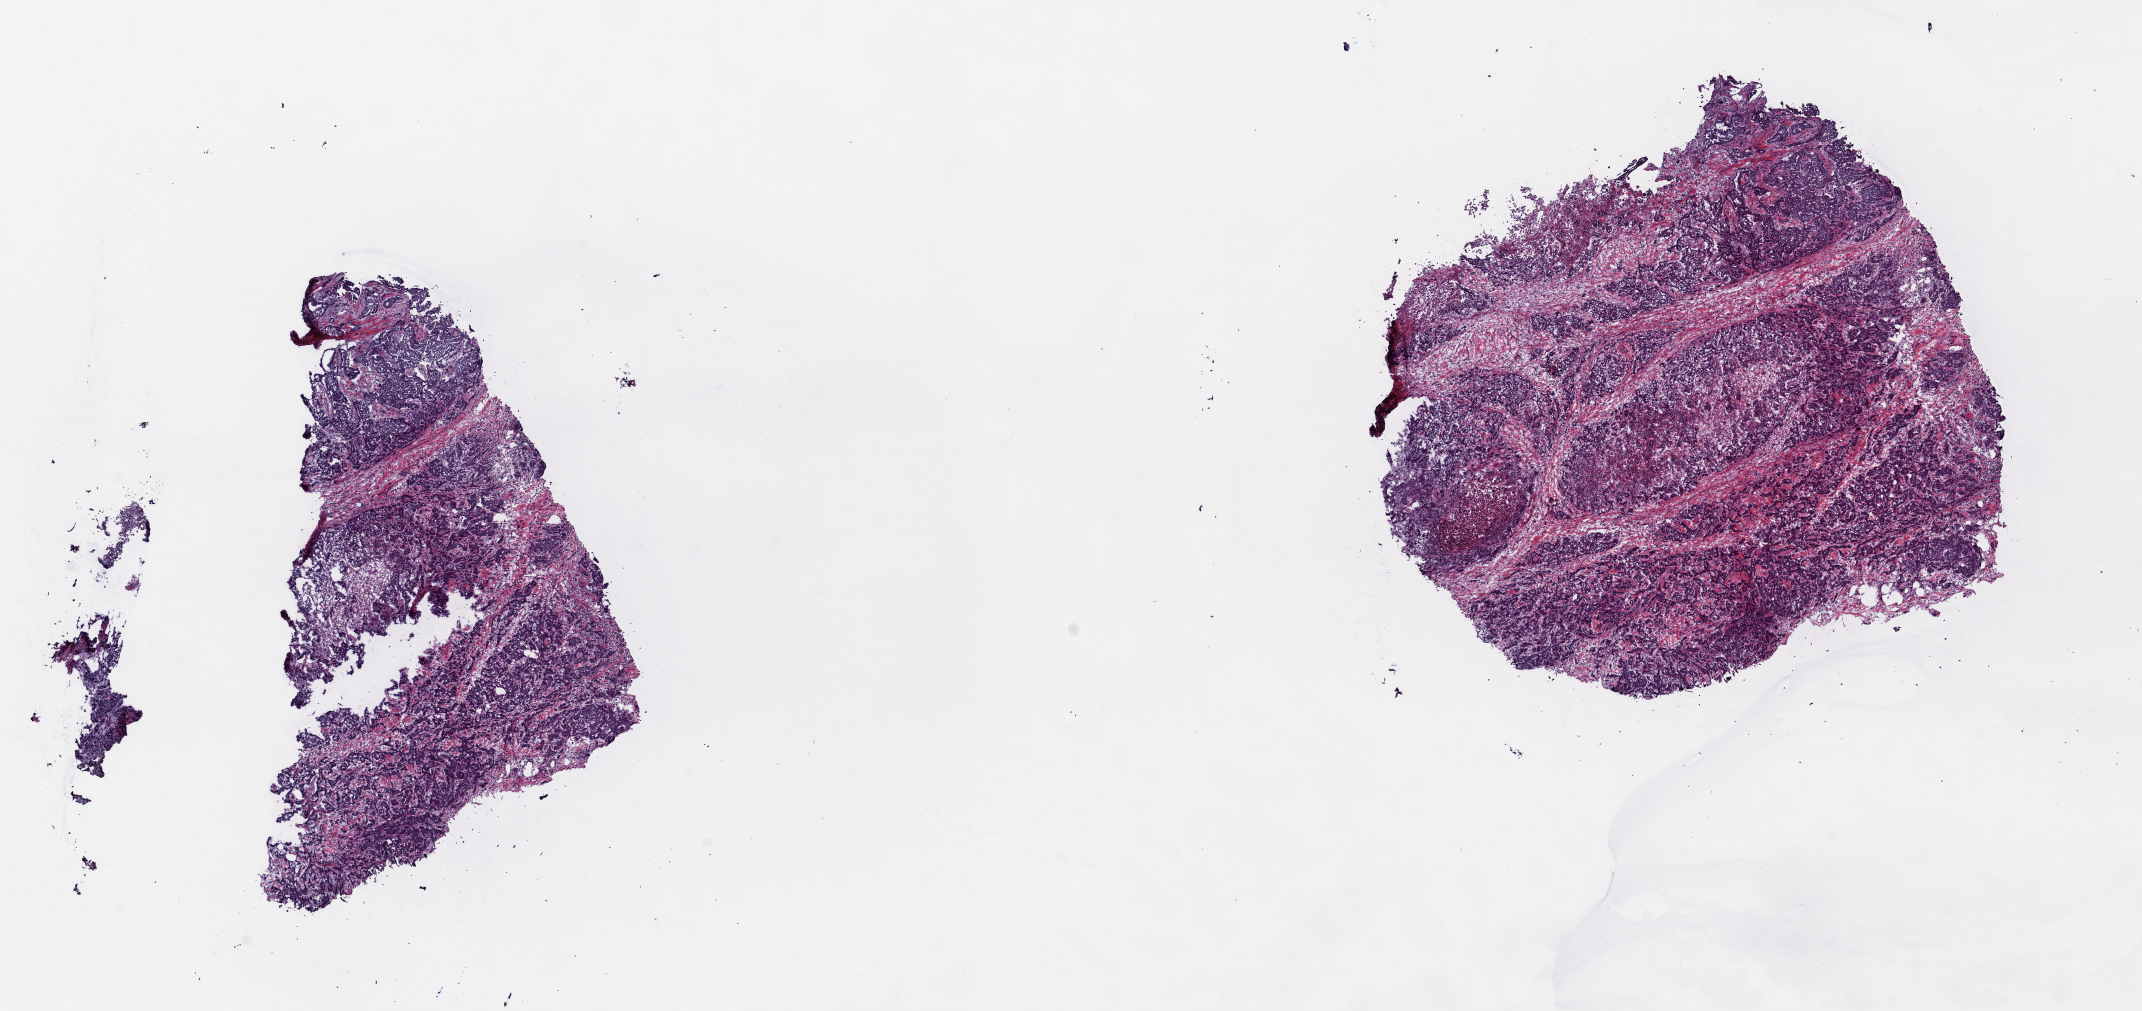
Whole-slide histology image, Hematoxylin and eosin (H&E) stained — a low-resolution overview of the entire scanned area, about 16.8 x 7.9 mm (from a 40x scan). Frozen section from the top of the tissue portion. Primary tumour sample from the breast. Female, age 66 years at initial diagnosis. Composition of this section per pathologist review: tumour cells 95%, tumour nuclei 90%, normal cells 0%, stromal cells 0%, necrosis 5%. Inflammatory infiltration, as recorded: lymphocyte infiltration 0%, monocyte infiltration 0%, neutrophil infiltration 0%.
• diagnosis: Infiltrating duct carcinoma, NOS
• TNM: T2 N1a M0
• AJCC pathologic stage: IIB